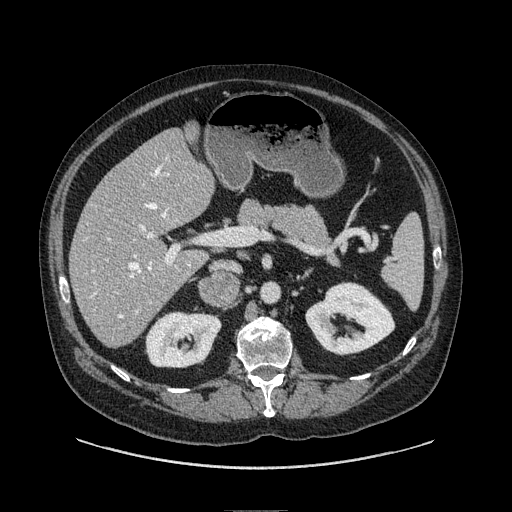
Contrast-enhanced abdominal CT, one axial slice. Slice 40 of 149 in the series (ordered by position). Soft-tissue window (W 400 / L 40 HU). 1.25 mm slice thickness. 512 × 512 image matrix, field of view 440 × 440 mm. Male patient. Case-level facts recorded for this patient, not image findings: diagnosis: adrenocortical carcinoma; tumour side: right adrenal; tumour size at pathology: 7.5 cm; Ki-67 index: 15 %.
Outlined on this slice (semi-automatic segmentation, software-assisted and operator-edited):
- mass: bounding box [x1, y1, x2, y2] px = [202, 275, 237, 303]